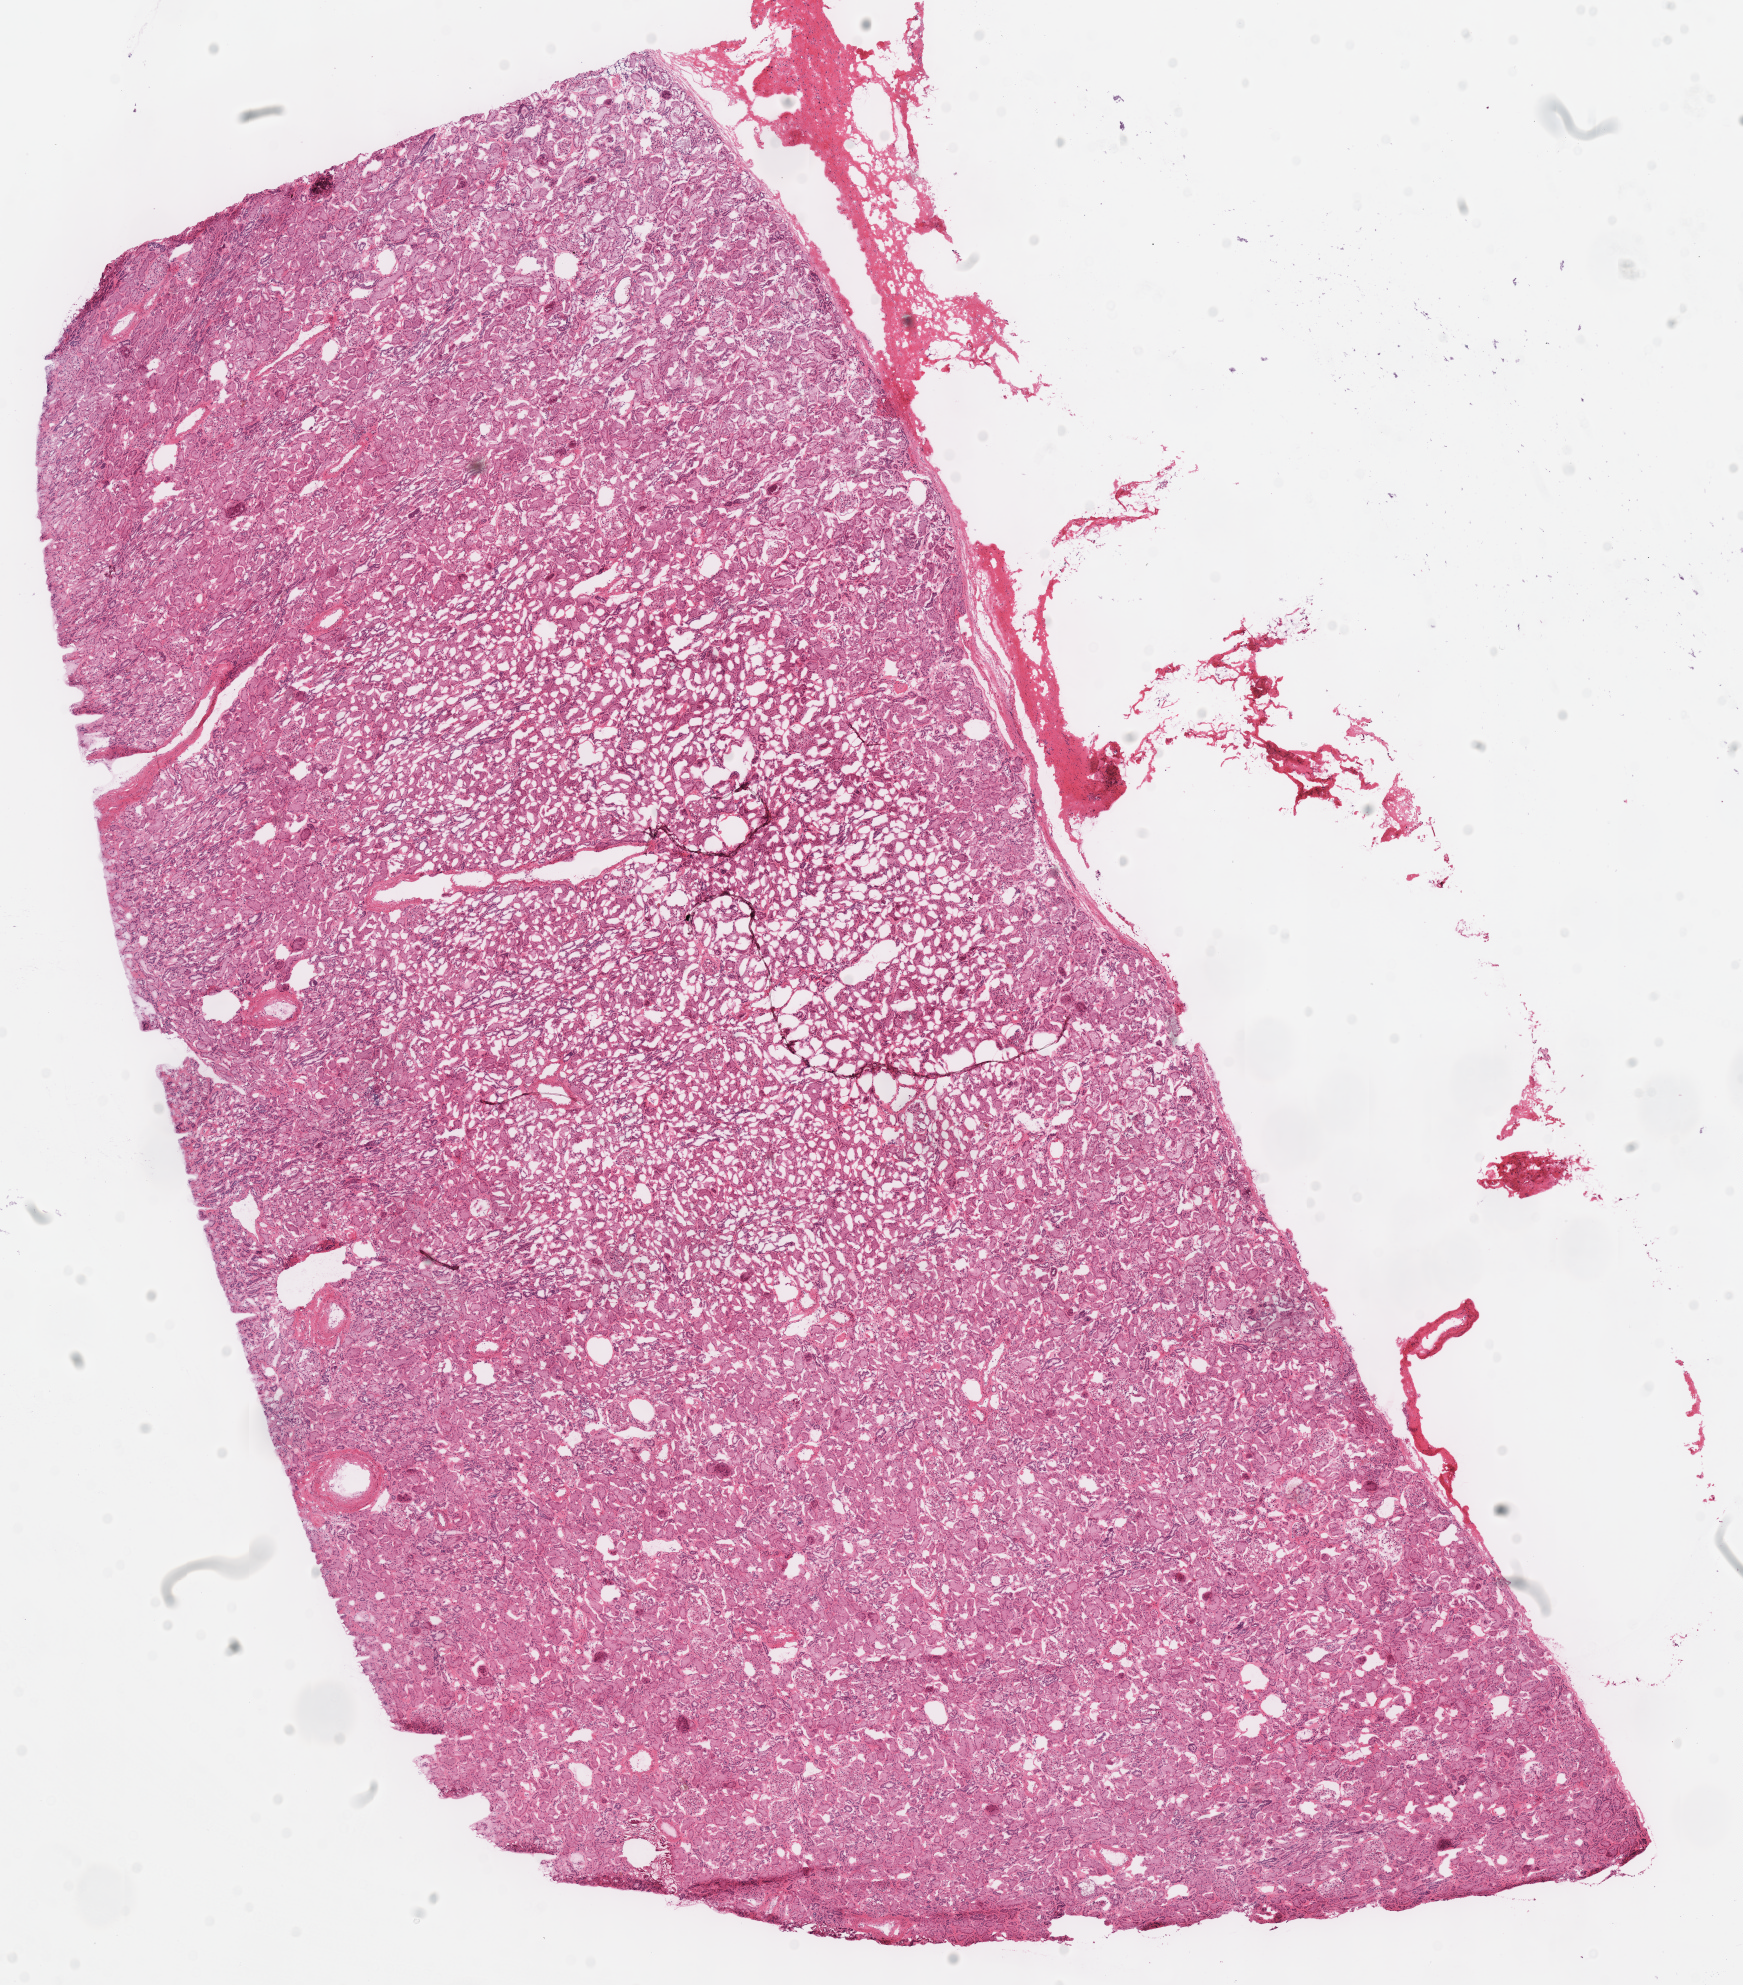
Whole-slide histology image, H&E-stained, whole scanned area (about 13.7 x 15.6 mm, from a 40x scan) shown as a low-resolution overview, frozen section from the top of the tissue portion, kidney, solid tissue normal (non-tumour tissue) sample. Male patient; age at initial diagnosis 51 years.
* this section: solid tissue normal (non-tumour) sample from the same patient
* patient diagnosis: Renal cell carcinoma, chromophobe type